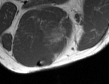
MRI of an extremity soft-tissue mass, one axial slice. MR volume resampled by the dataset authors to the PET/CT grid (not the native acquisition matrix). 109 × 84 image matrix. Male patient. Case-level facts recorded for this patient, not image findings: histological type: synovial sarcoma; site of the primary tumour: left poplietal fossa.
Outlined on this slice (expert contour drawn on MRI and transferred to this co-registered scan by the dataset authors):
- gross tumour volume (mass): bounding box [x1, y1, x2, y2] px = [41, 33, 51, 49]